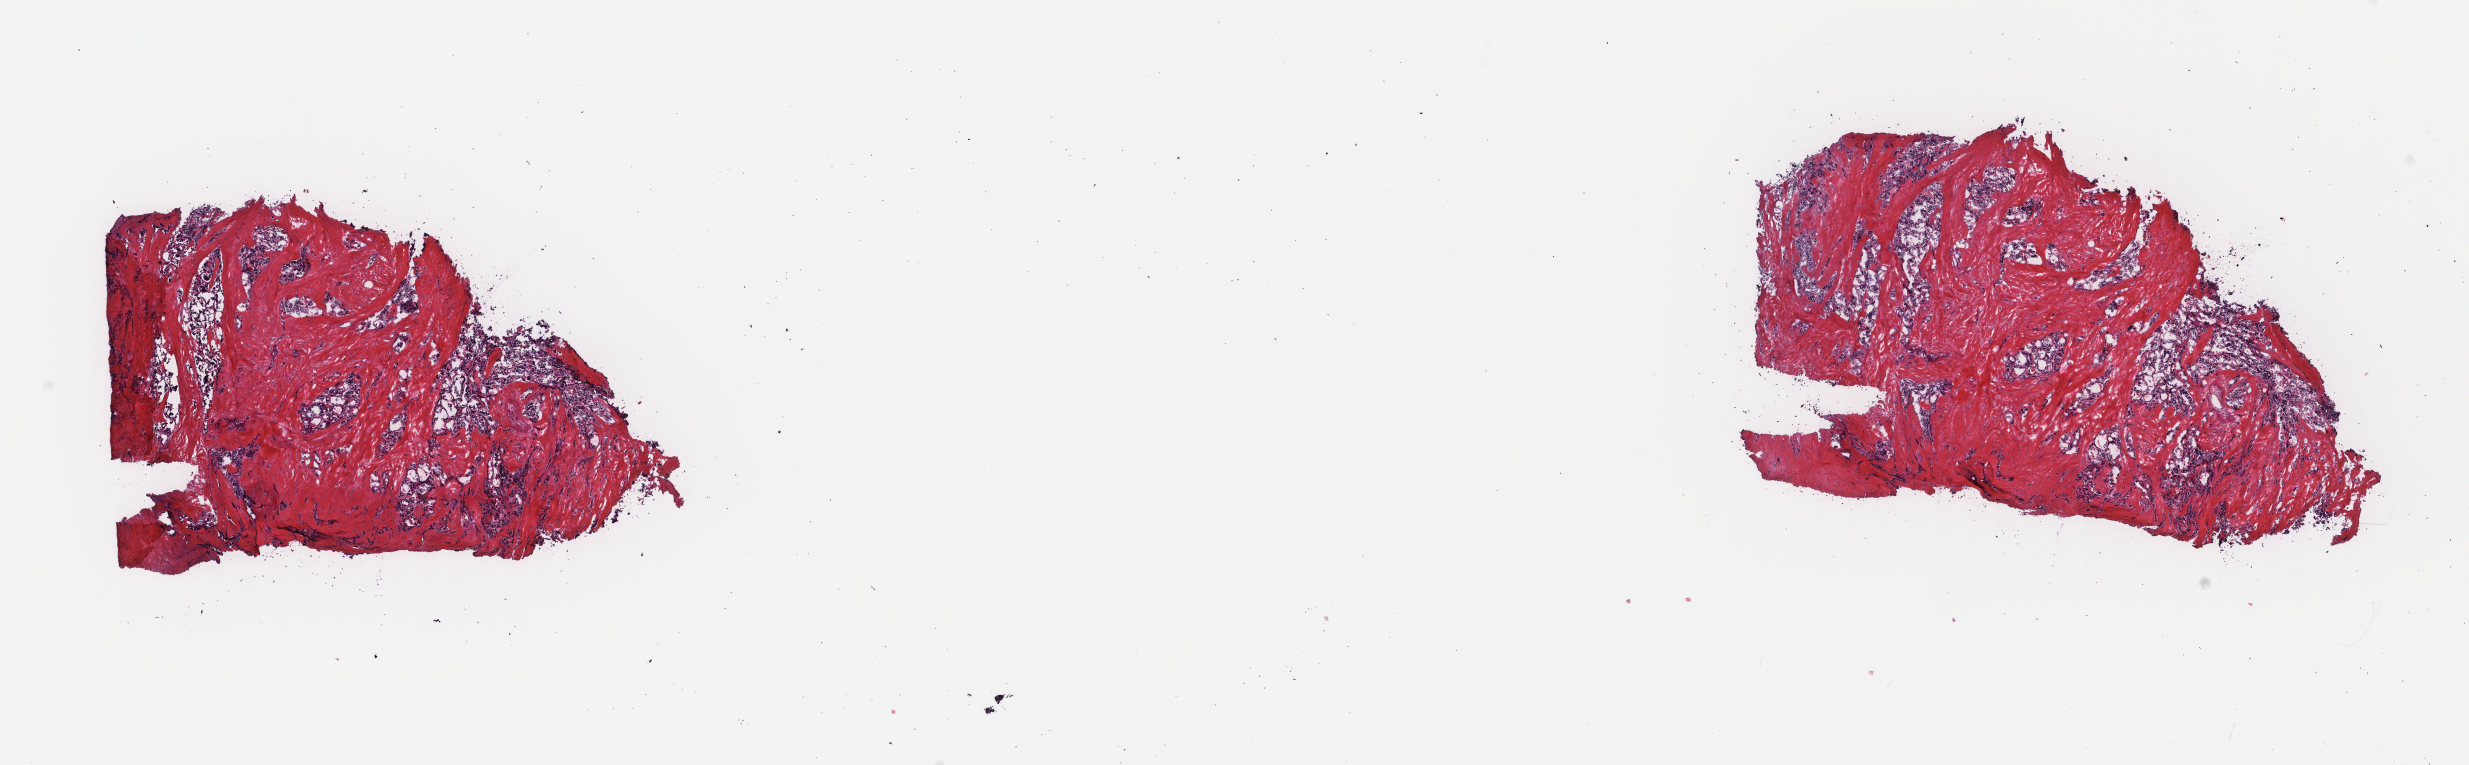
H&E whole-slide image, a low-resolution overview of the entire scanned area, about 19.6 x 6.1 mm (from a 40x scan); frozen section from the top of the tissue portion; primary tumour sample from the thyroid. Male, age 61 years at initial diagnosis. Pathologist review of this section (percent, as recorded): tumour cells 40%, tumour nuclei 65%, normal cells 10%, stromal cells 50%, necrosis 0%. Inflammatory infiltration, as recorded: lymphocyte infiltration 1%, monocyte infiltration 1%, neutrophil infiltration 0%.
Diagnosis: Papillary adenocarcinoma, NOS. Laterality: left. TNM: T4 N1b M0. AJCC pathologic stage: III.